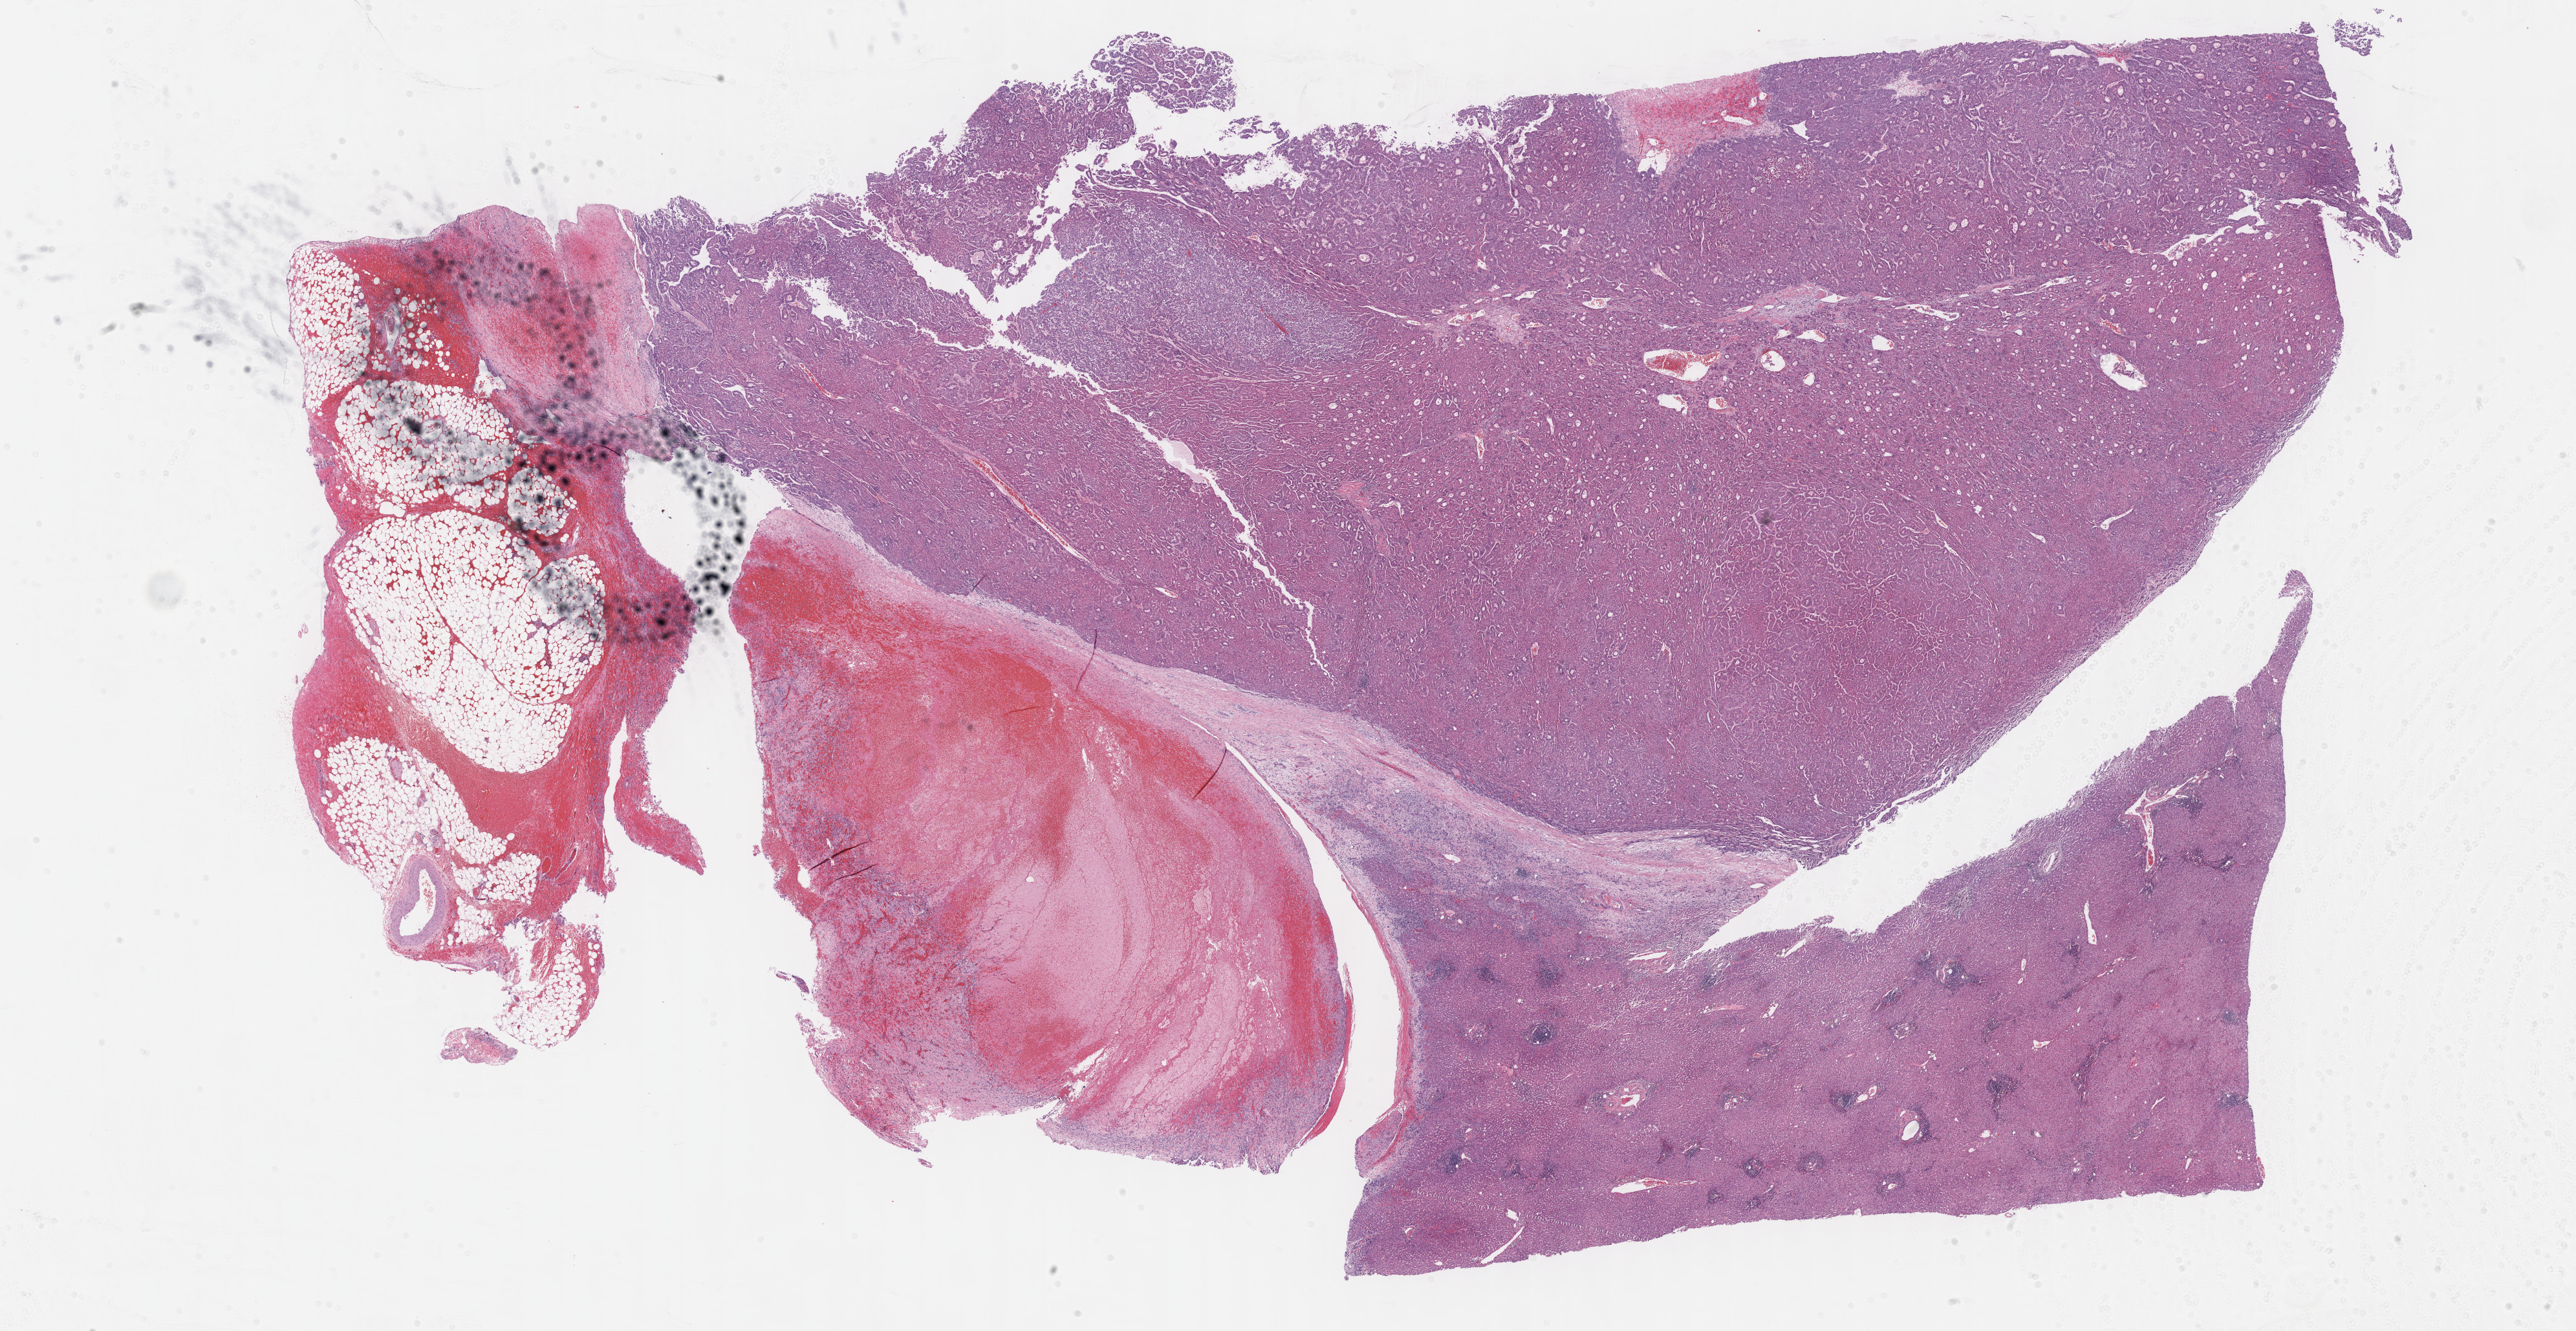
Digitized H&E tissue section (whole slide) — low-resolution overview of the scanned area, about 32.2 x 16.6 mm (acquisition: 40x scan). Formalin-fixed paraffin-embedded (FFPE) diagnostic section. Liver, primary tumour sample. Patient: male, age at initial diagnosis 61 years.
Histologic diagnosis: Hepatocellular carcinoma, NOS.